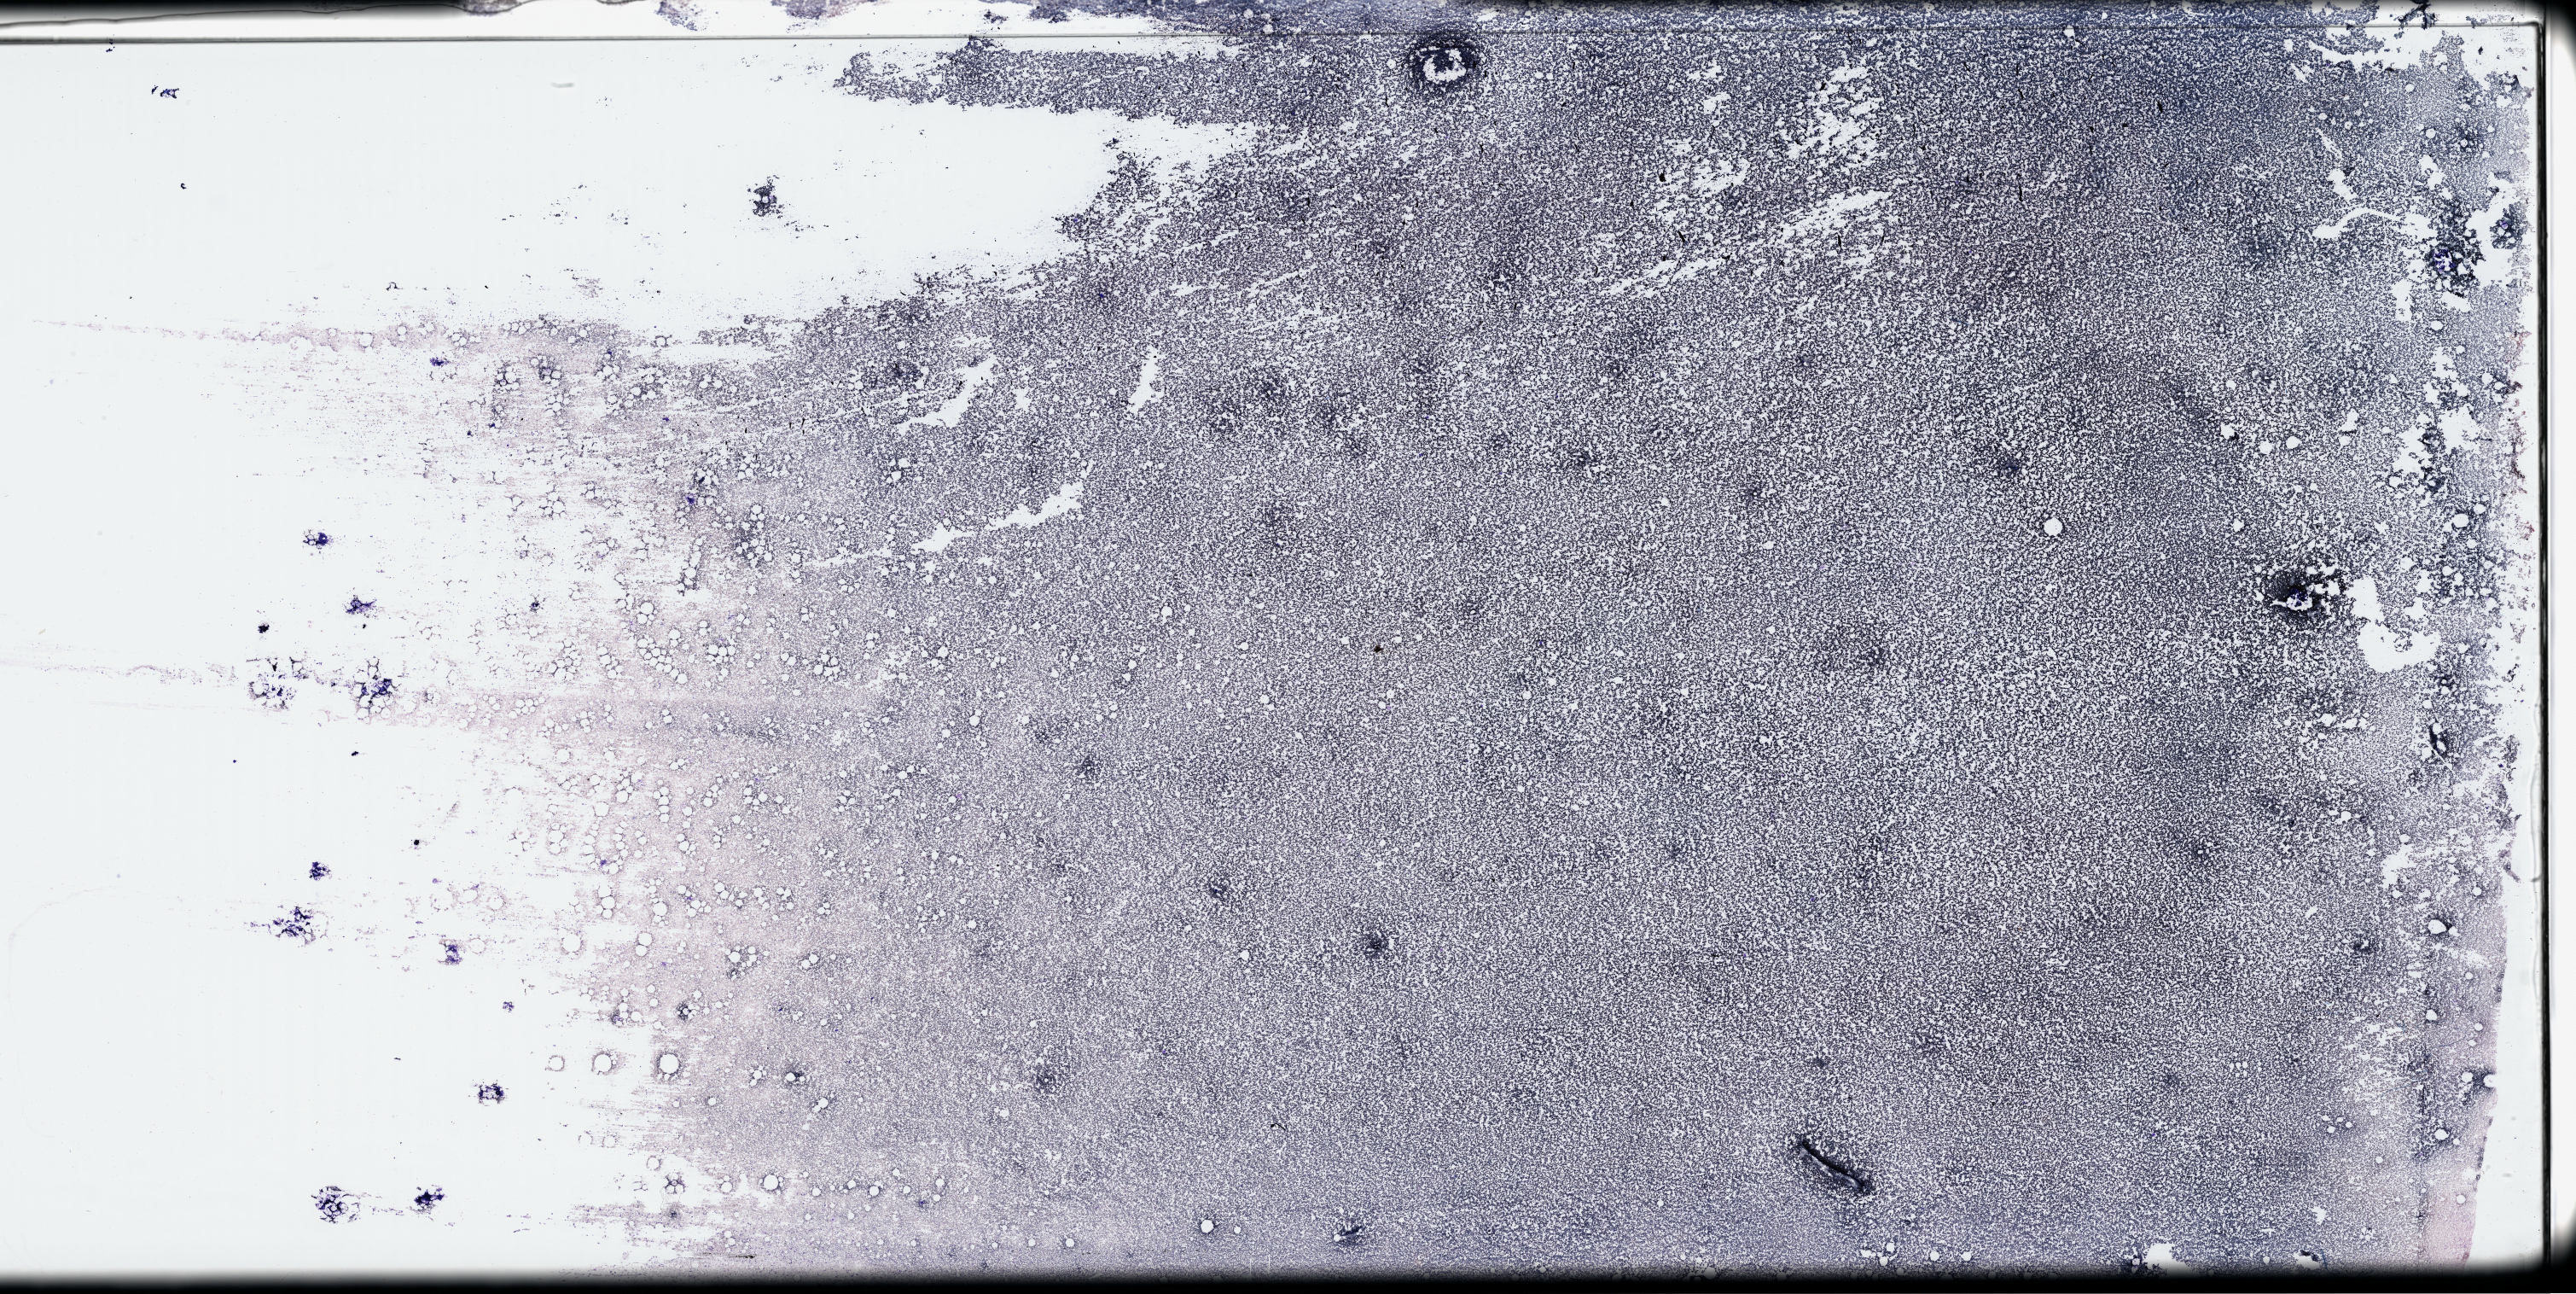
Digitized Hematoxylin and eosin (H&E) stained tissue section (whole slide) — whole scanned area (about 48.8 x 24.5 mm, from a 40x scan) shown as a low-resolution overview, peripheral blood (leukaemic) sample. 60-year-old female patient.
• diagnosis: Acute Myeloid Leukemia
• FAB classification: M5
• WHO classification: Acute monoblastic and monocytic leukemia